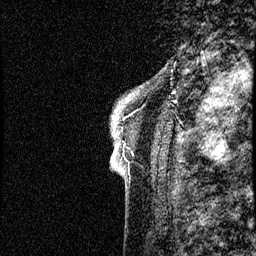
Breast MRI (dynamic contrast-enhanced), one sagittal slice. Slice 3 of 60 in the series (ordered by position). Dynamic contrast-enhanced study with each time point stored as its own series, time point 2 of 4 at this slice position (early post-contrast, ordered by acquisition time). 1.5 T. TE 4.2 ms, TR 17.6 ms. 256 × 256 image matrix, field of view 200 × 200 mm. Patient: female, 40 years. From the clinical record (not read from this slice): setting: breast cancer imaged before/during neoadjuvant chemotherapy; receptor status: HER2-positive.
Outlined on this slice (semi-automatically segmented with operator editing):
- analysis volume of interest (the breast-tissue region the enhancement analysis was run in; not a lesion): box from (x=106, y=55) to (x=183, y=206) px
- tumour enhancement mask (voxels above the 100 % enhancement threshold inside the analysis volume of interest): (x=115, y=148)–(x=117, y=150)